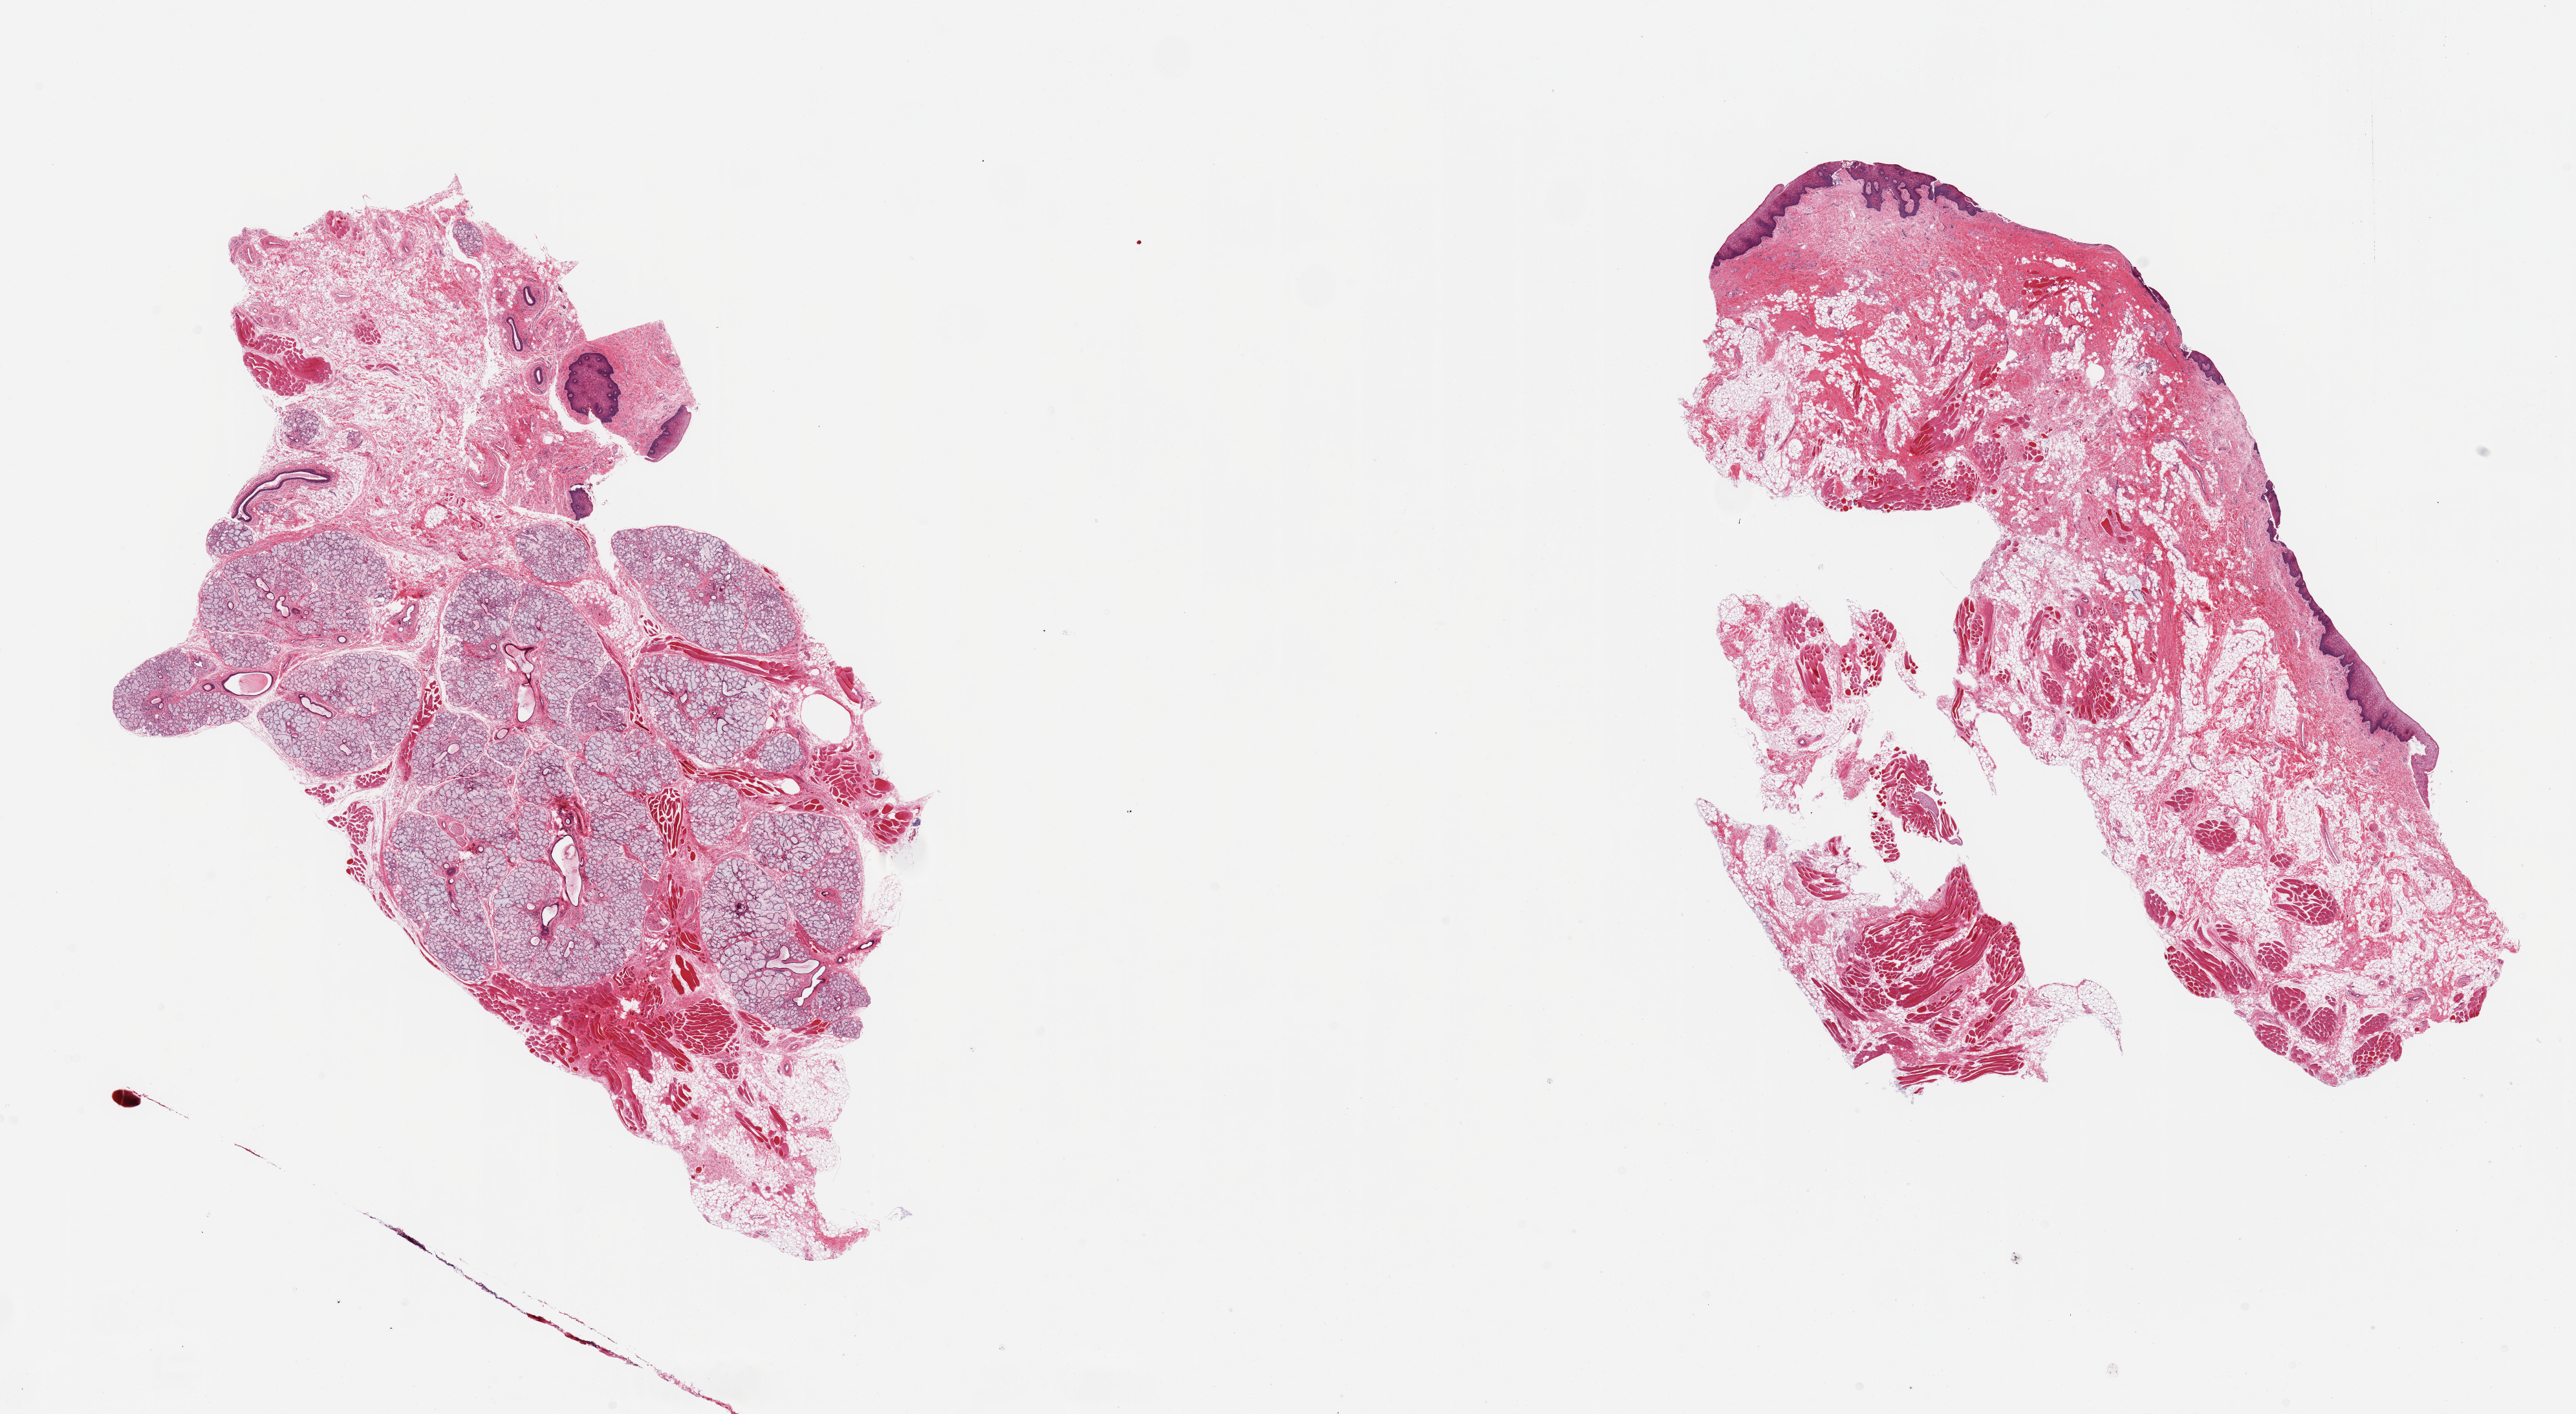
Whole-slide image, haematoxylin and eosin stain, brightfield, shown as a low-resolution overview of the whole scanned area (about 31.5 x 17.3 mm, acquisition: 20x scan). Female donor.
Specimen: PAXgene-fixed paraffin-embedded (PFPE) section; target tissue: minor salivary gland; donor tissue sample.